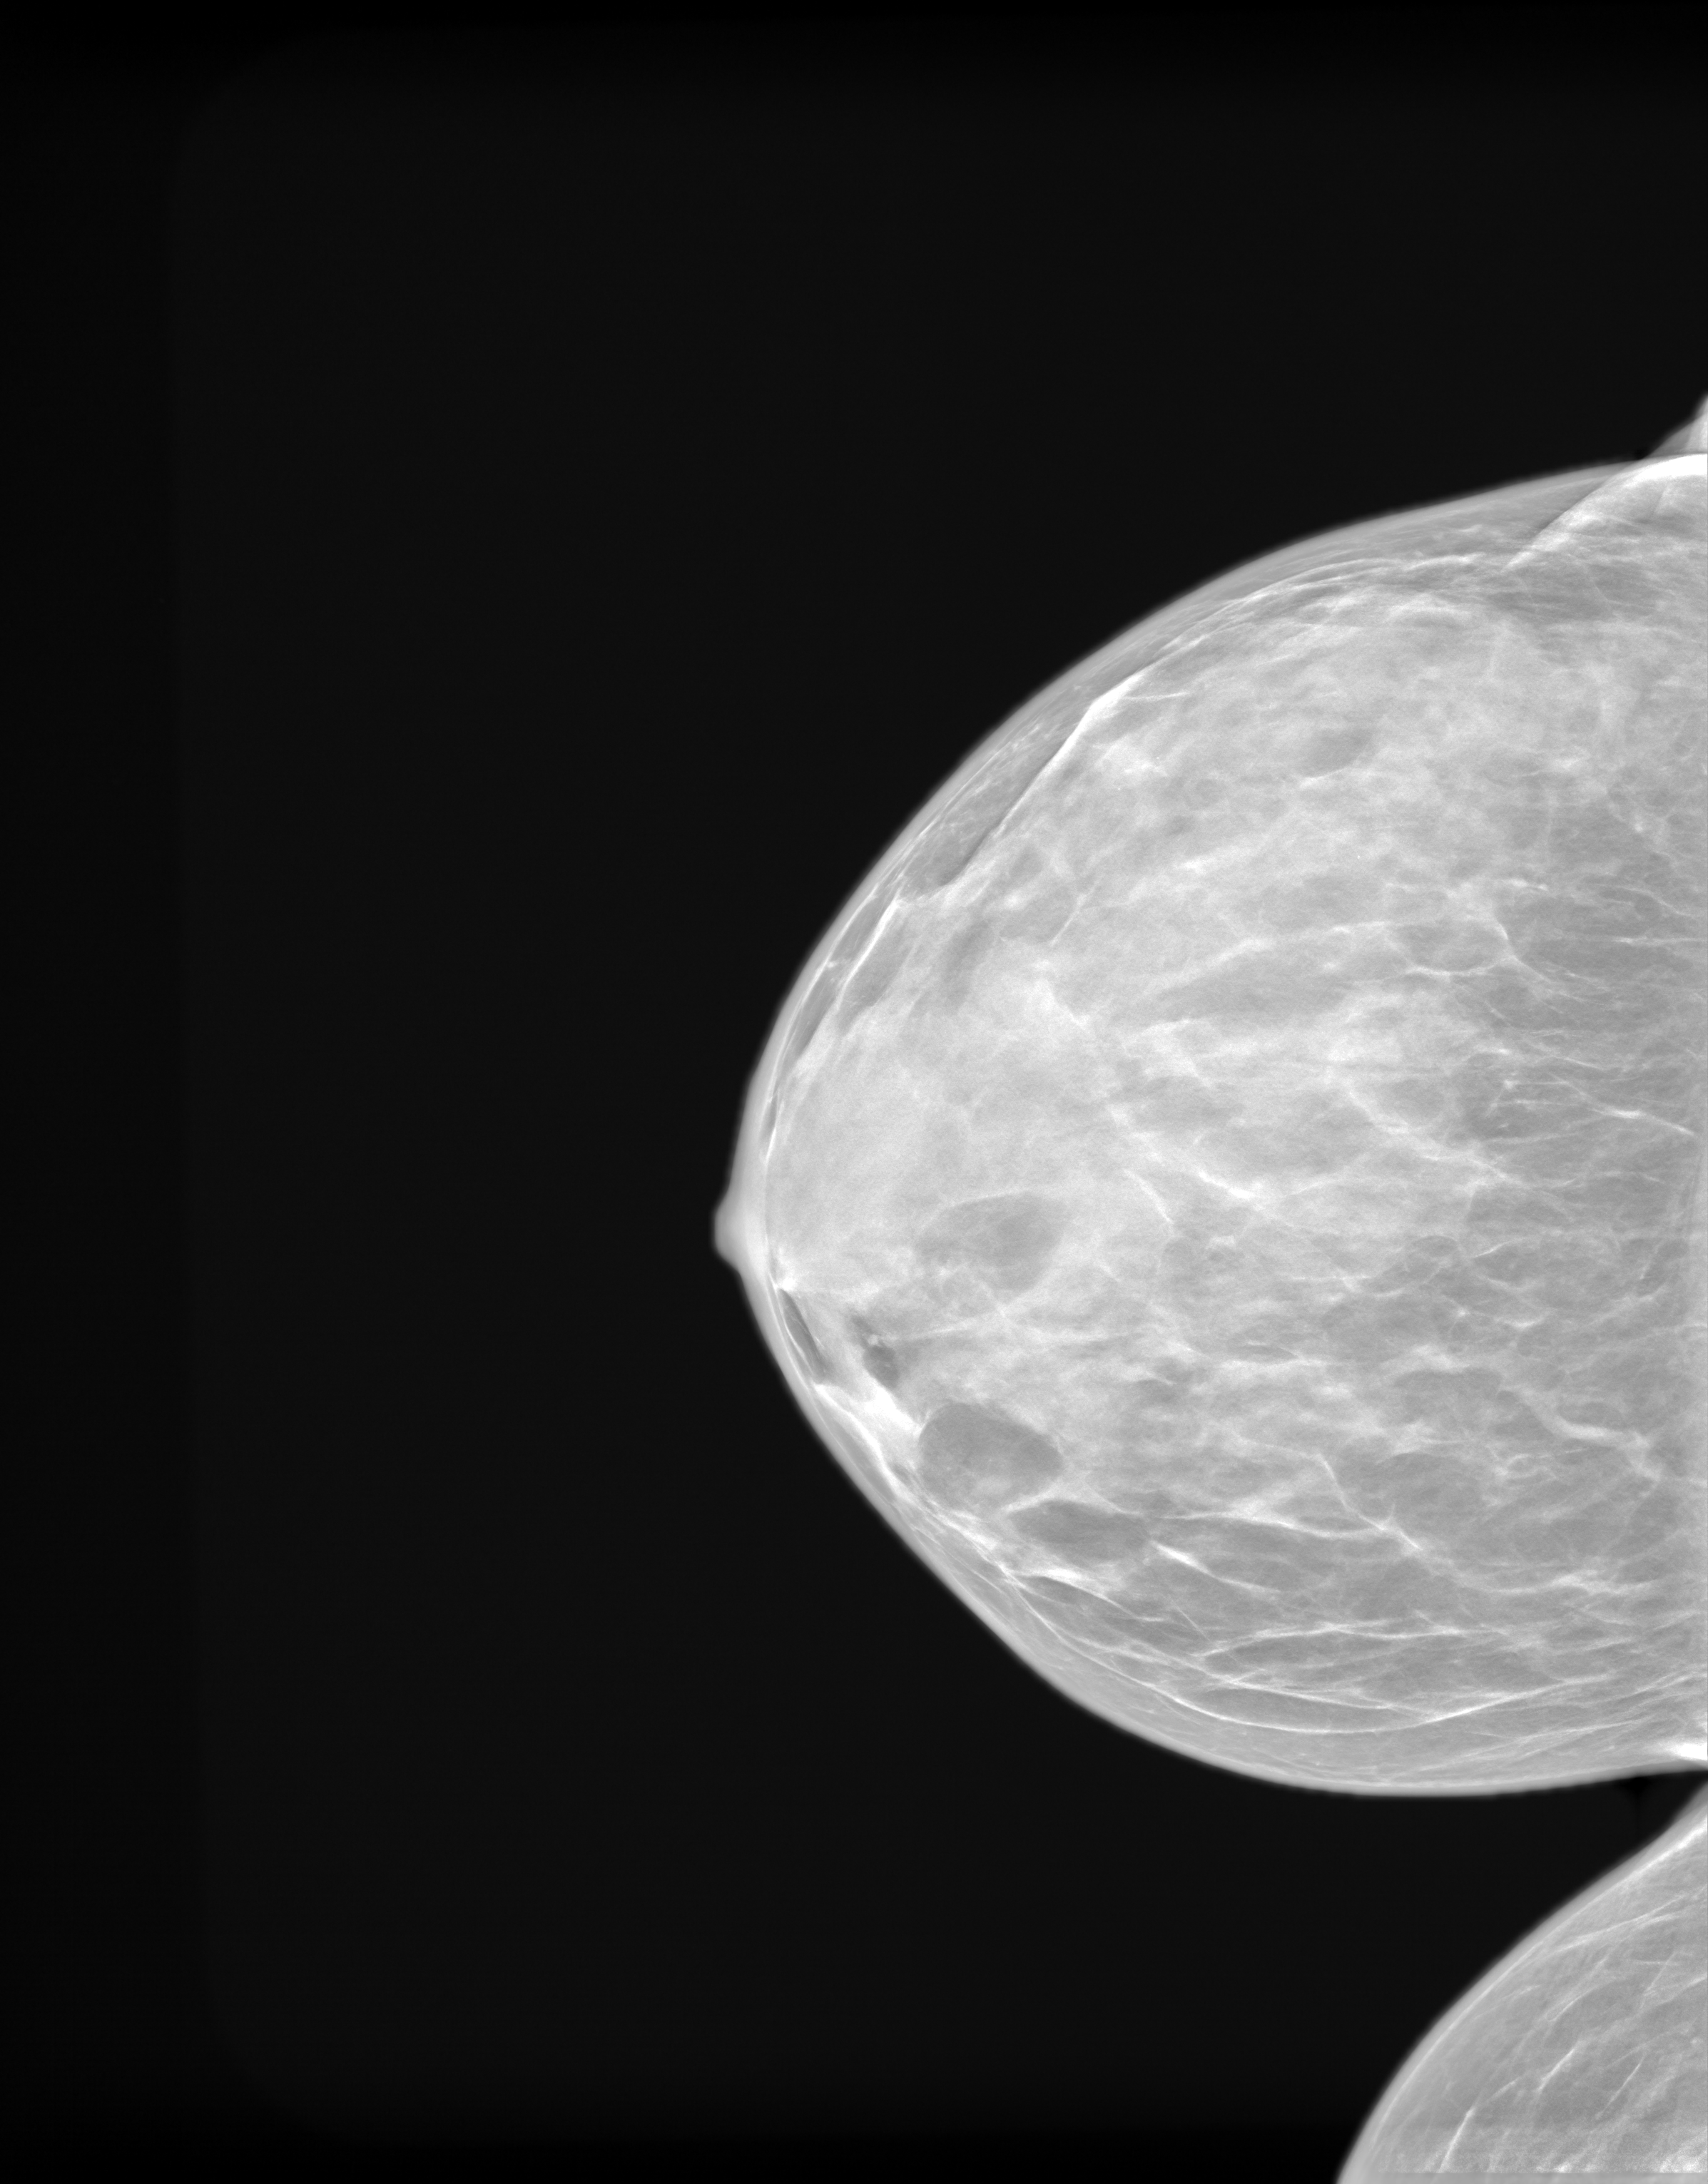
Annual screening mammography examination. Patient aged 48 years (female).
Image type: synthesized 2-D view from tomosynthesis. Breast: right. Projection: craniocaudal (CC) view.